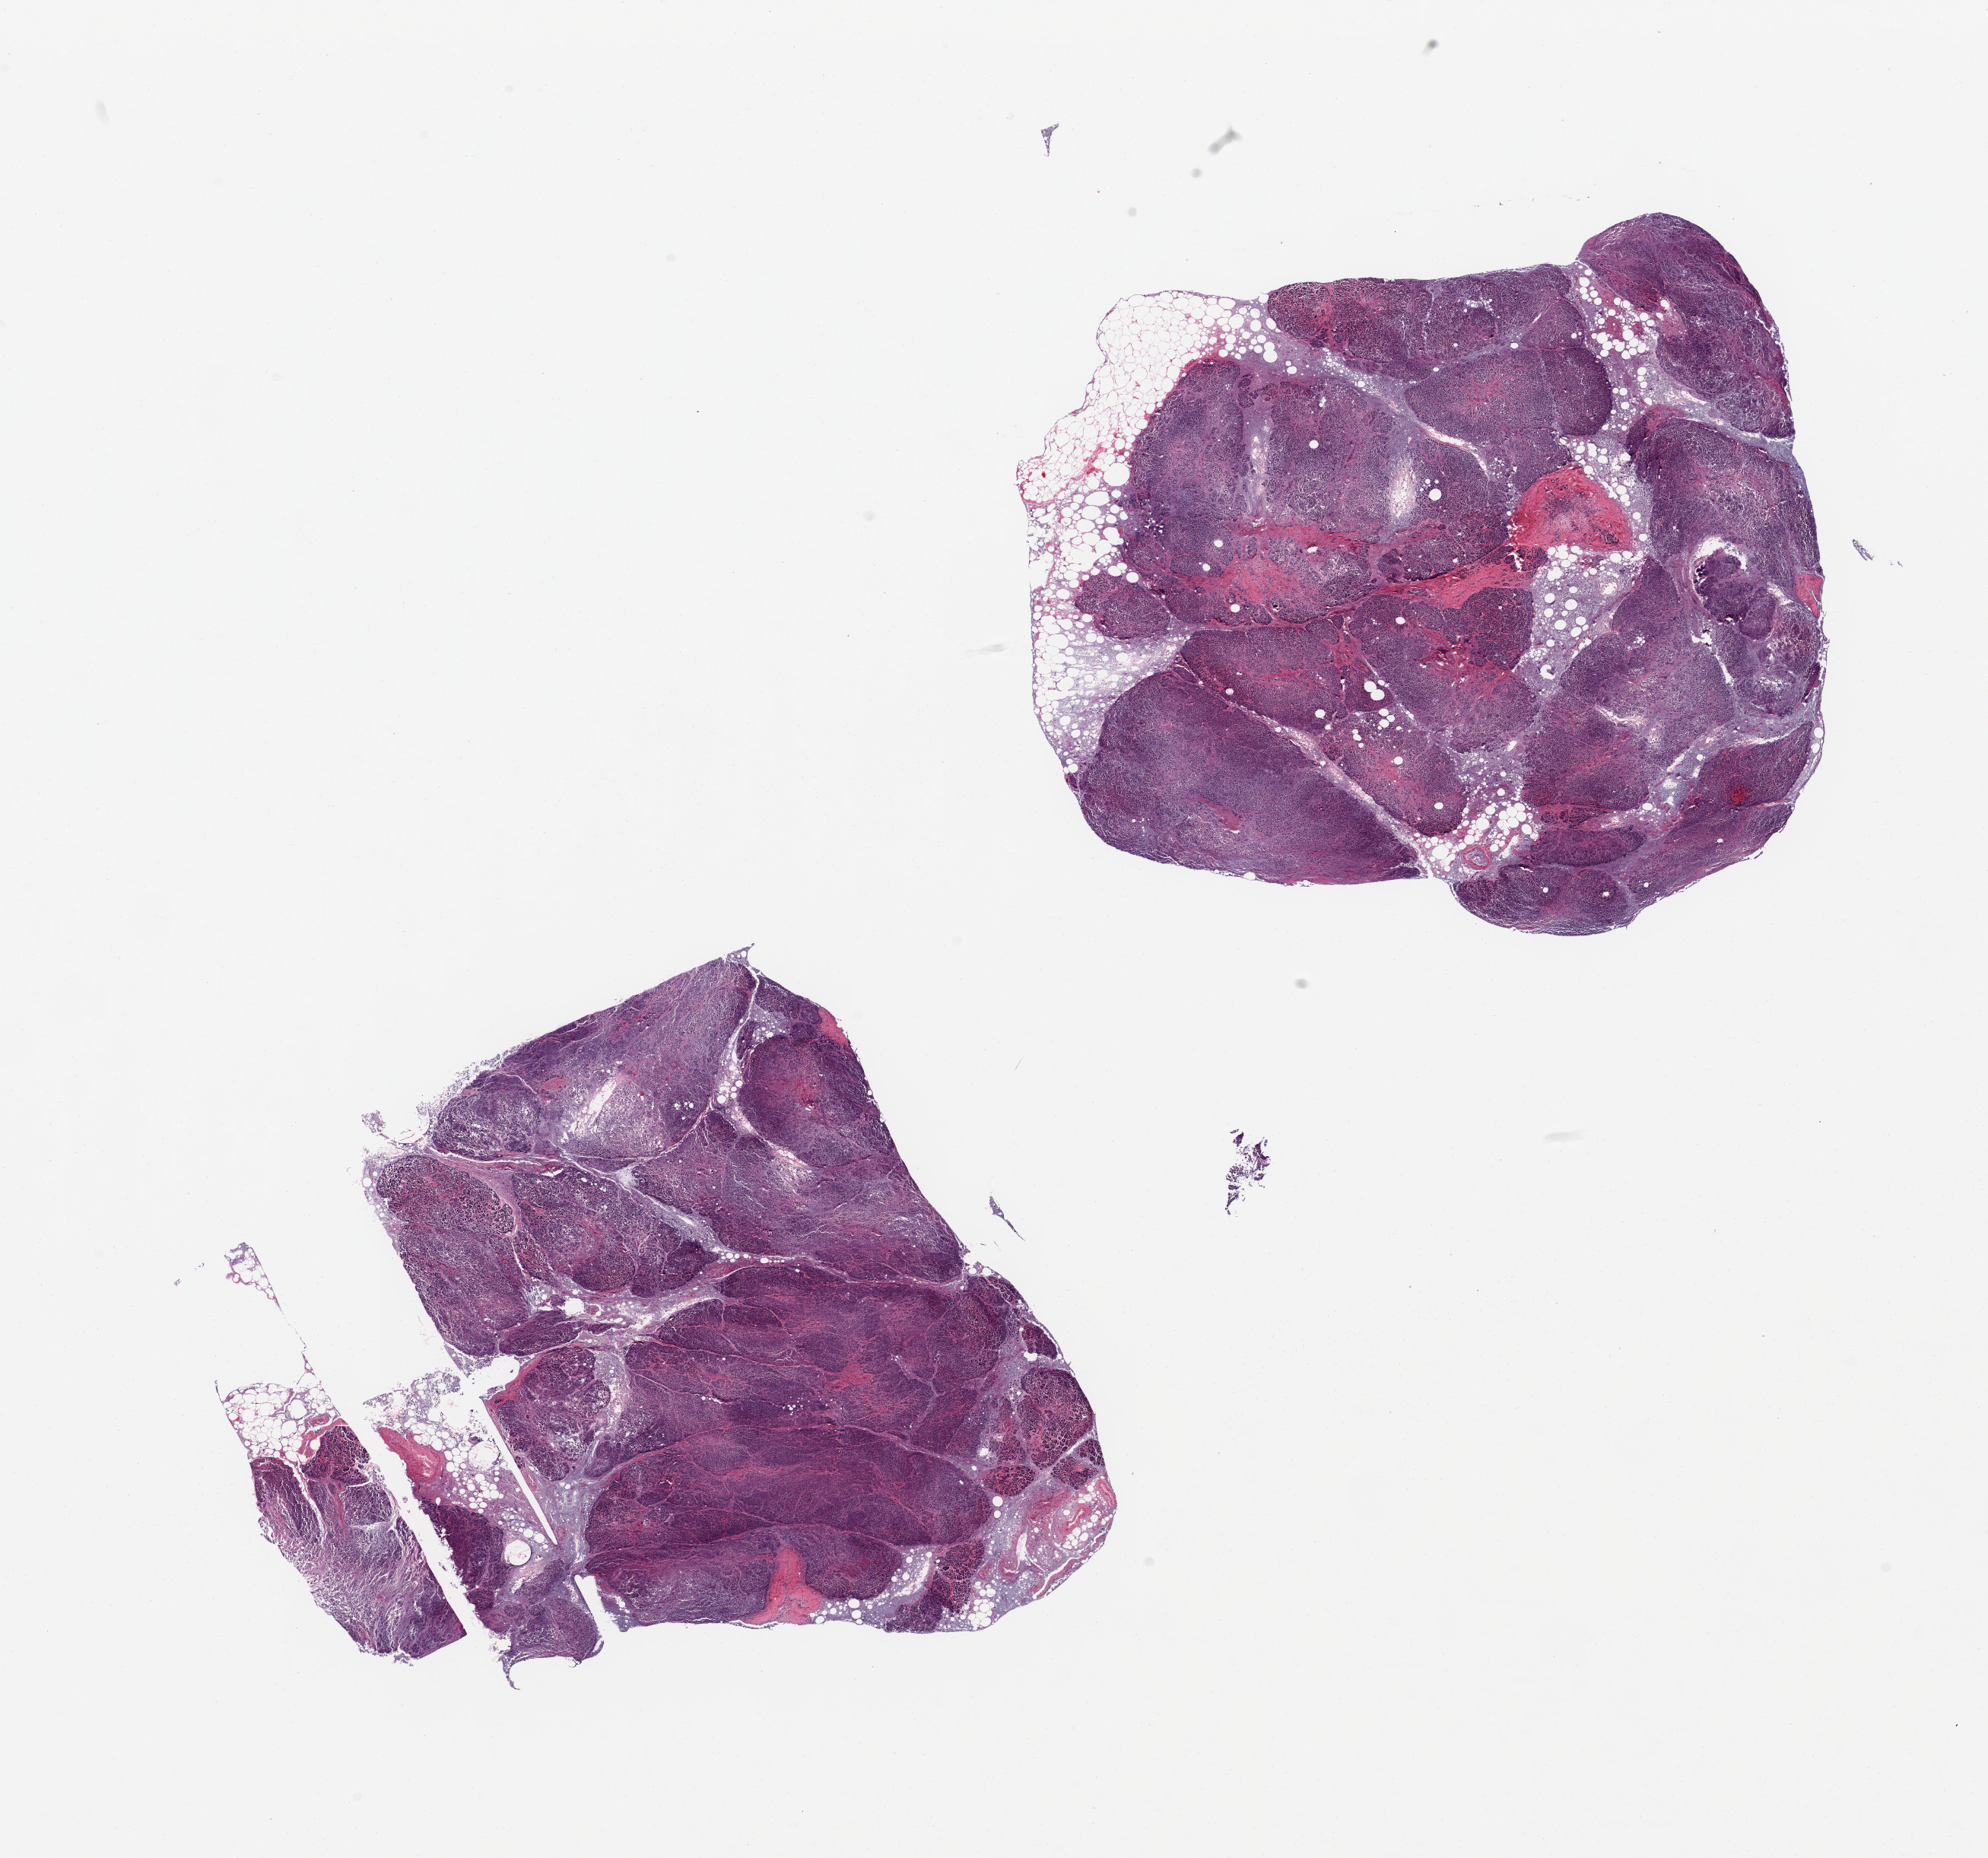
H&E whole-slide image, brightfield — low-resolution overview of the scanned area, about 20.7 x 19.3 mm. PAXgene-fixed paraffin-embedded (PFPE) section. Sampled site (target tissue): pancreas. Tissue donor sample. Female donor.
Review note (as recorded): 2 pieces, severe autolysis/saponification.